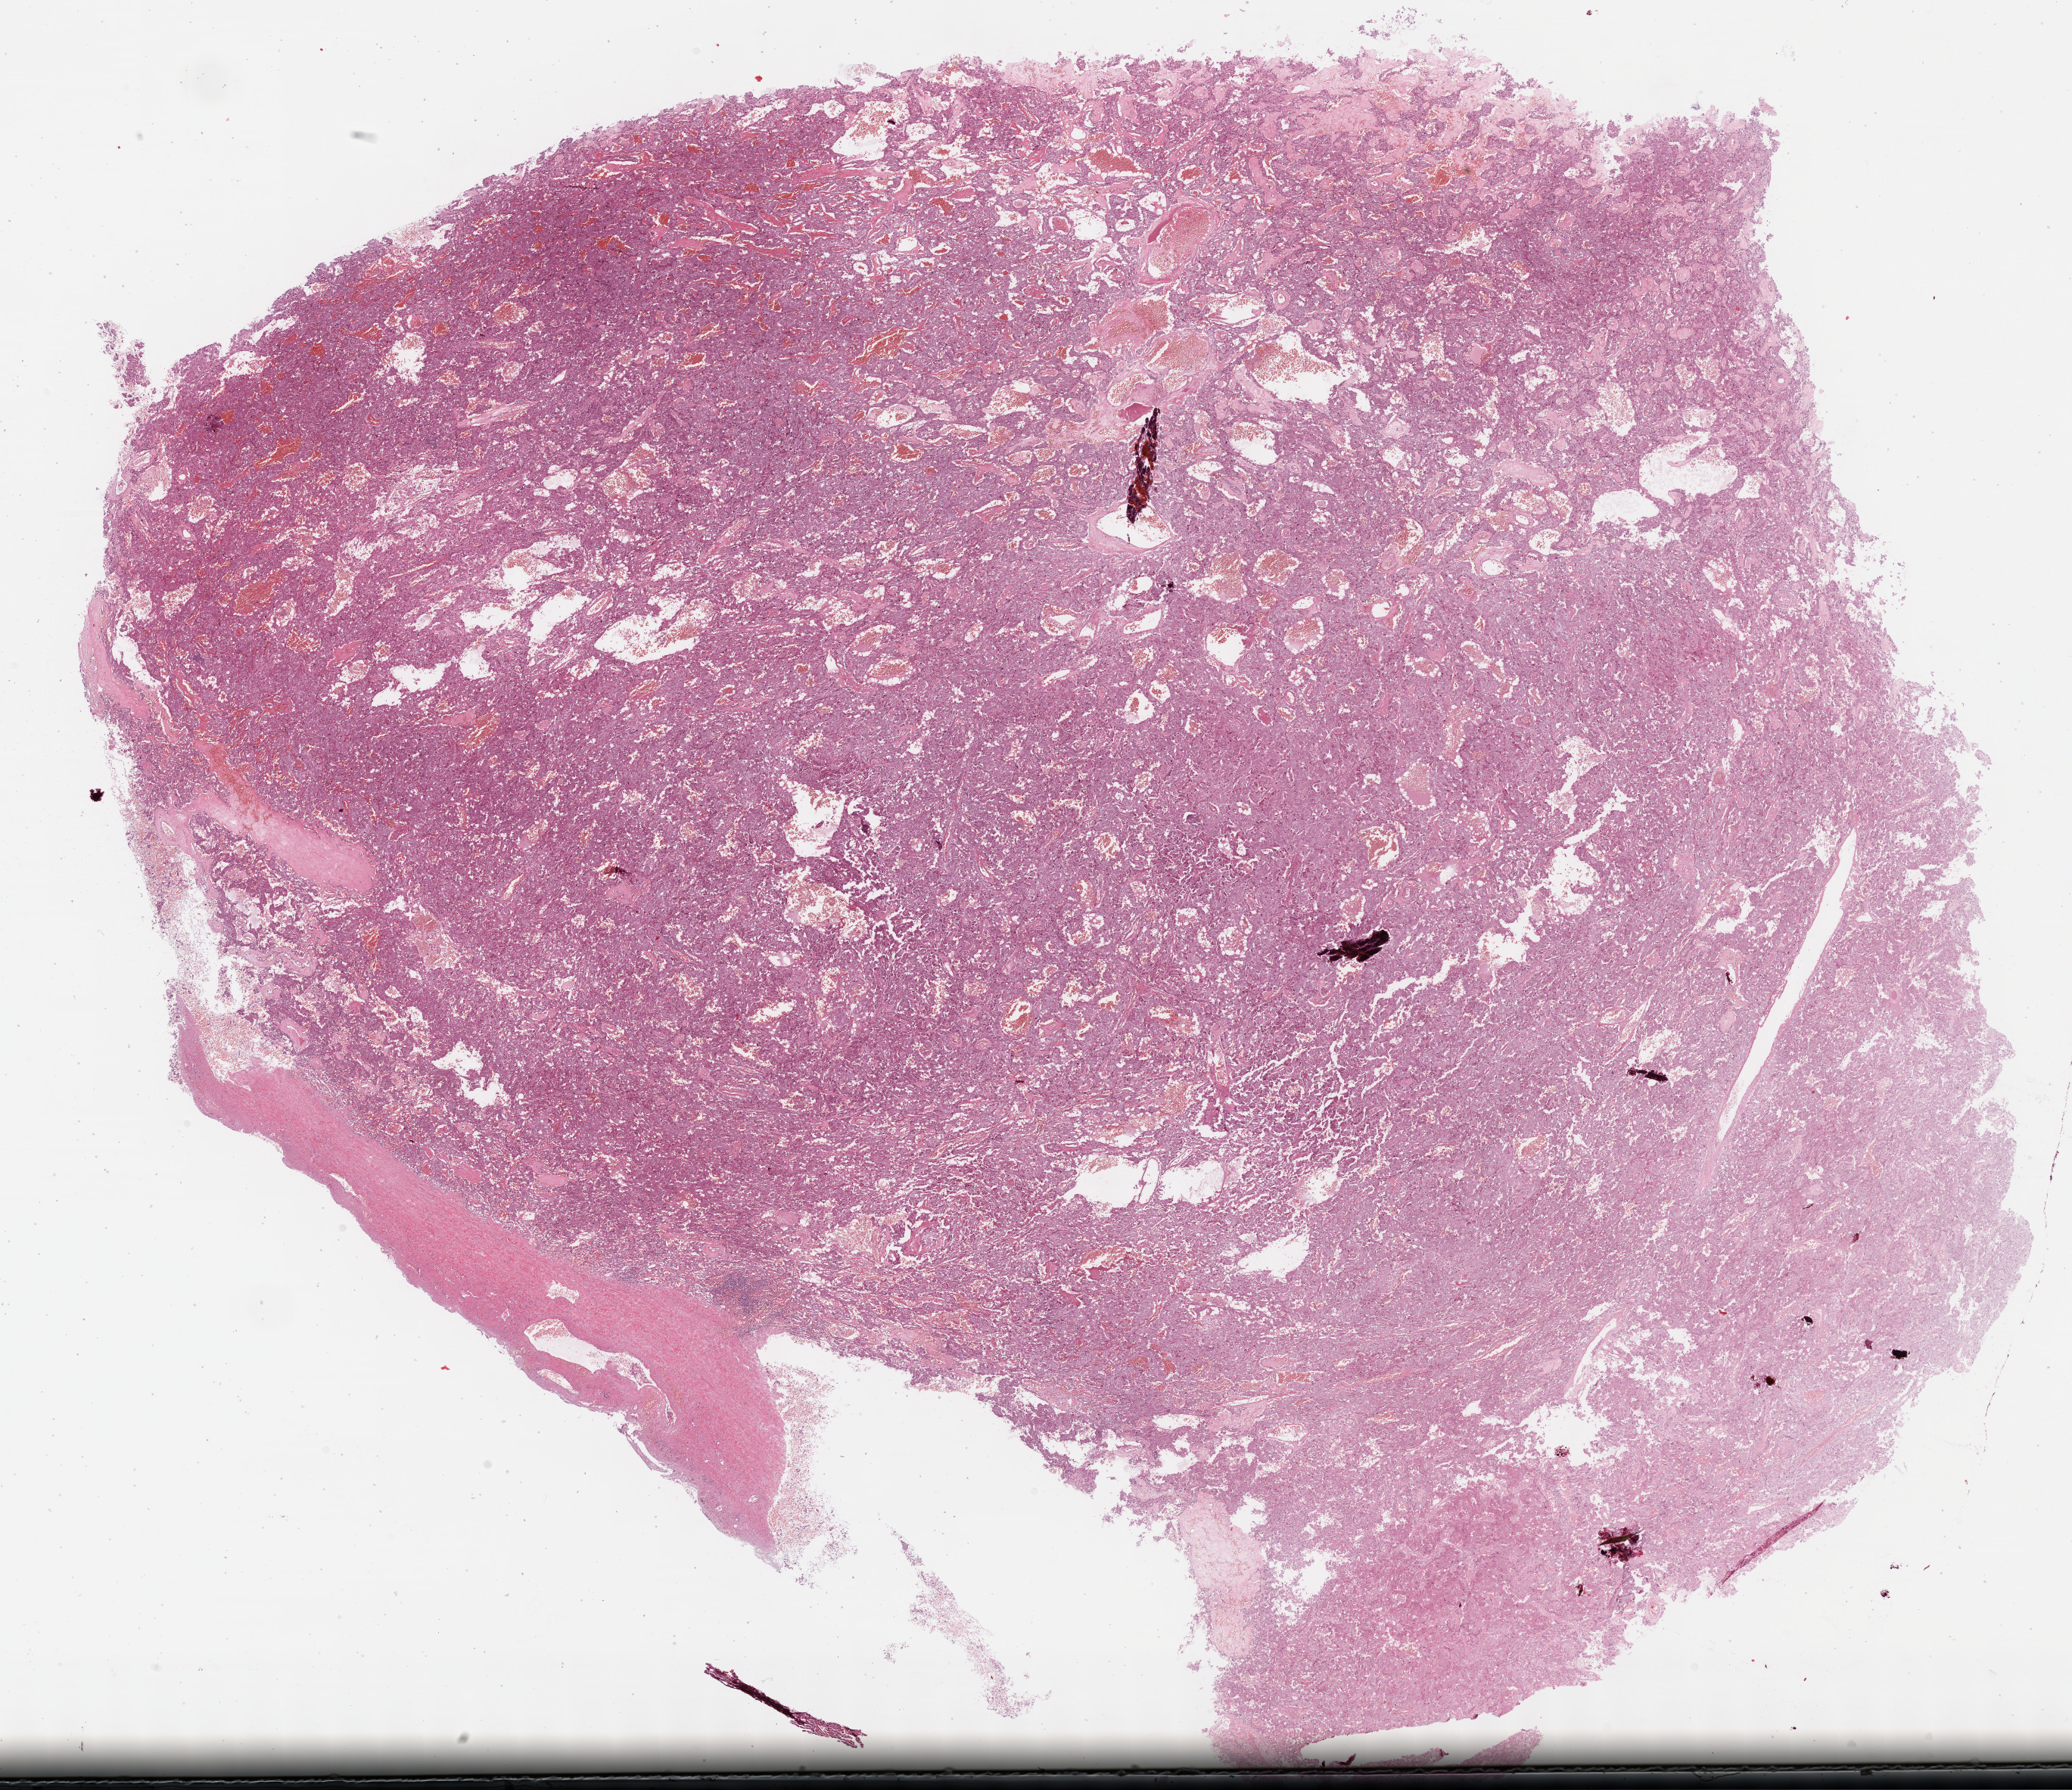
H&E-stained whole-slide image, shown as a low-resolution overview of the whole scanned area (about 22.1 x 19.1 mm, from a 40x scan), formalin-fixed paraffin-embedded (FFPE) diagnostic section, primary tumour sample from the adrenal gland. Male, age 59 years at initial diagnosis.
Pathologic diagnosis: Pheochromocytoma, malignant. Laterality: right.